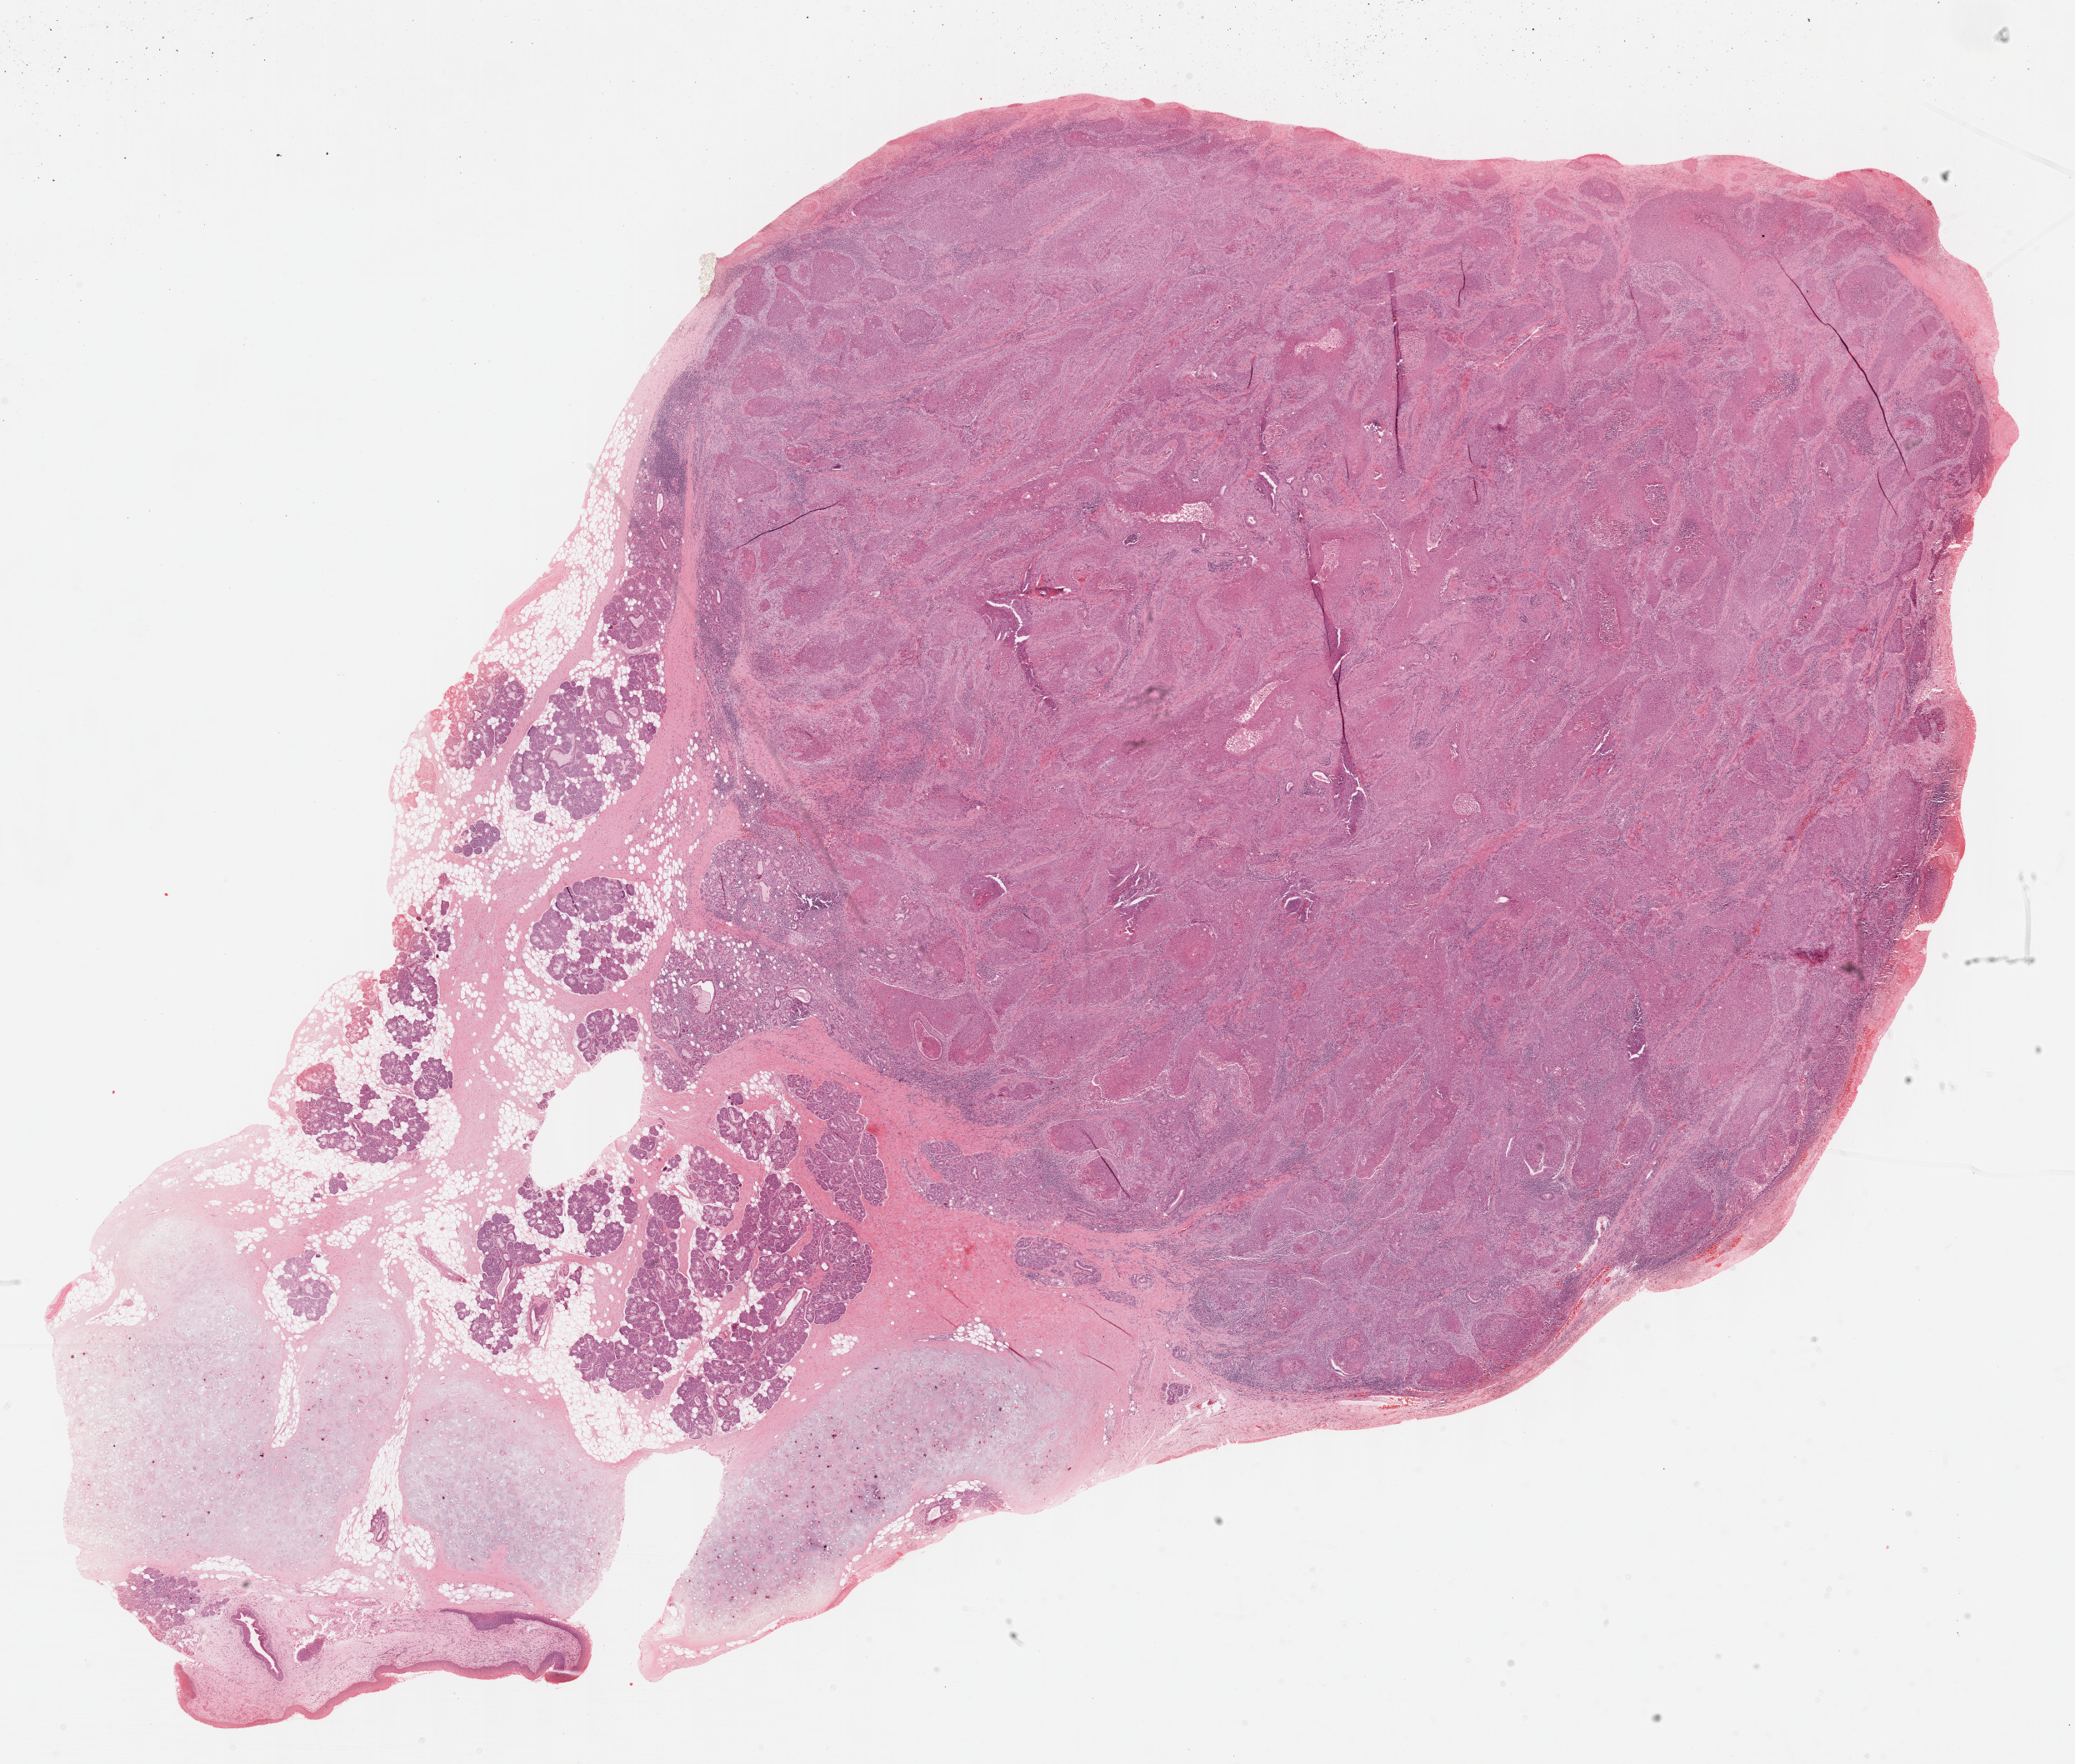
Hematoxylin and eosin (H&E) stained whole-slide image — low-resolution overview of the scanned area, about 20.1 x 17.1 mm; formalin-fixed paraffin-embedded (FFPE) diagnostic section; primary tumour sample from the head and neck. Male patient; age at initial diagnosis 61 years.
Diagnosis: Squamous cell carcinoma, NOS (larynx, NOS).